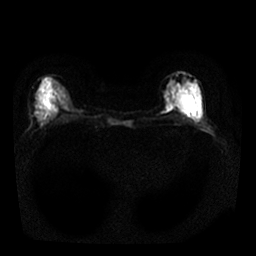
Breast MRI, one axial slice; slice 9 of 25 in the series (ordered by position); diffusion-weighted series; image 2 of 4 stored at this slice position (different b-values; order by instance number); 1.5 T; 256 × 256 image matrix, field of view 320 × 320 mm. Female patient.
Outlined on this slice (outlined manually by an expert reader):
- tumour on diffusion-weighted imaging: bounding box <183,95,195,111> (left, top, right, bottom; pixels)